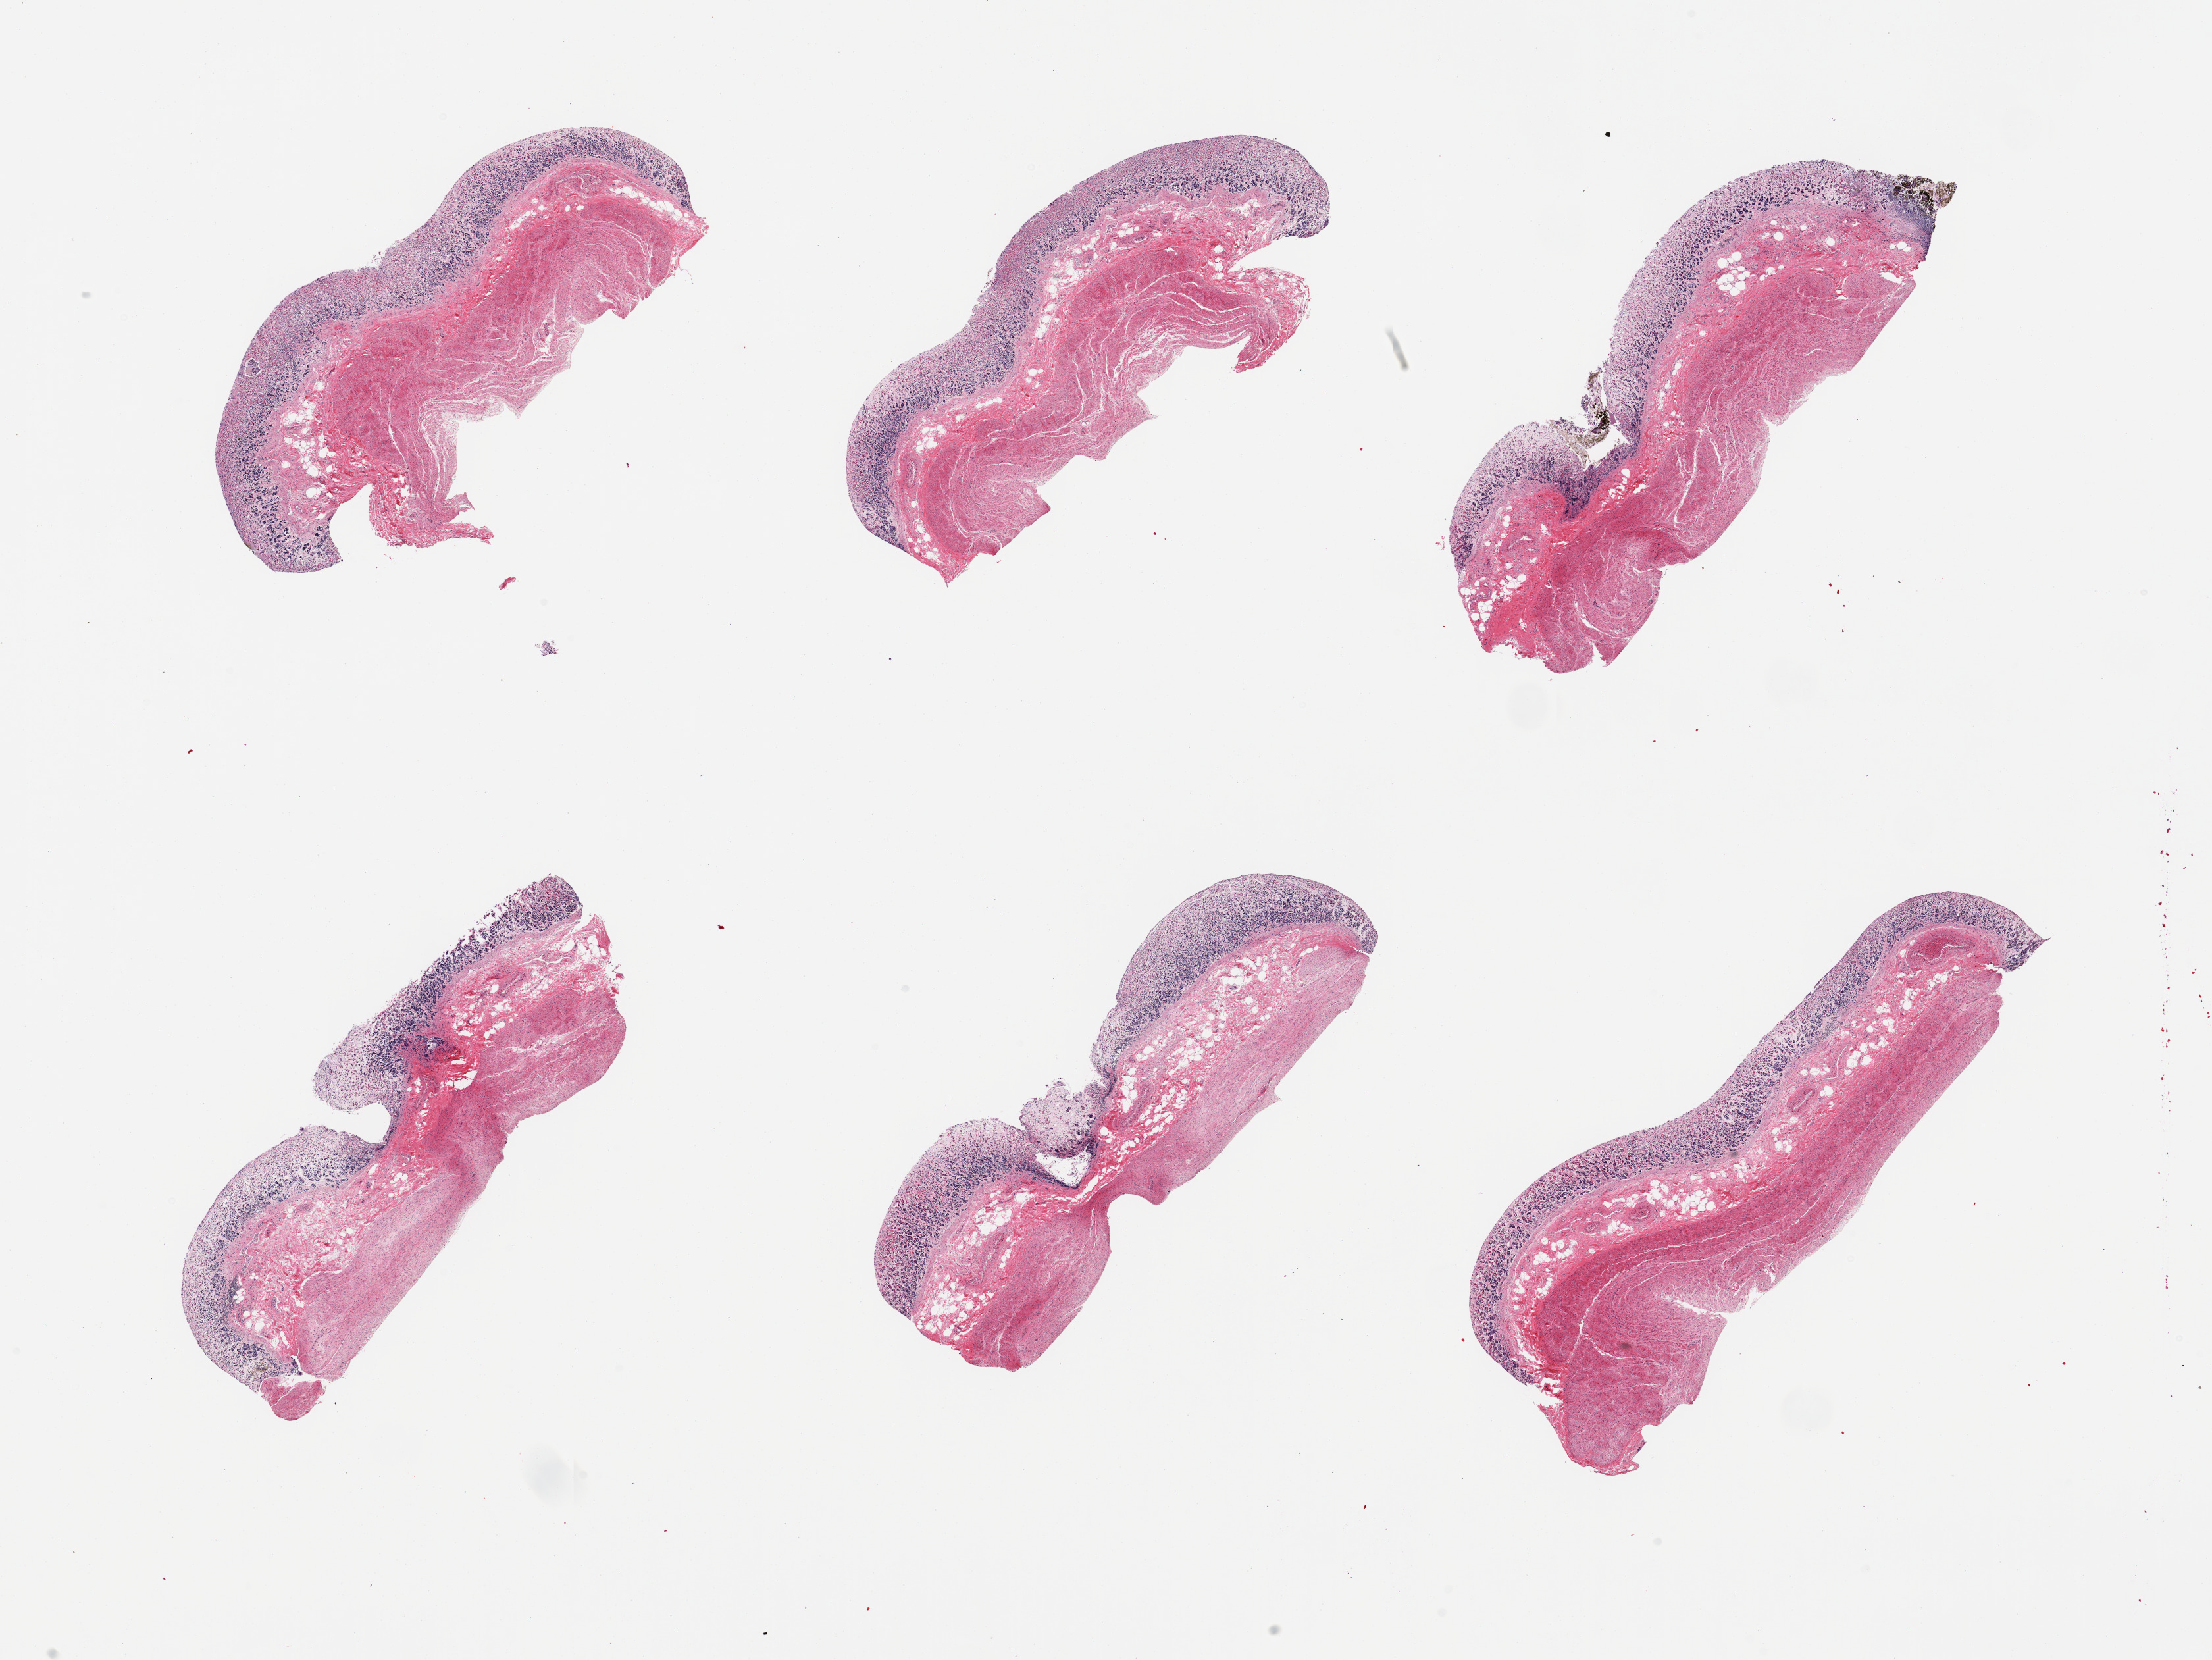
Whole-slide image, haematoxylin and eosin stain — shown as a low-resolution overview of the whole scanned area (about 26.6 x 19.9 mm, slide scanned at 20x); PAXgene-fixed, paraffin-embedded tissue; sampled site (target tissue): stomach; tissue donor sample.
- reviewer comment on this tissue sample: 6 pieces mucosa up to ~0.75mm, advanced autolysis